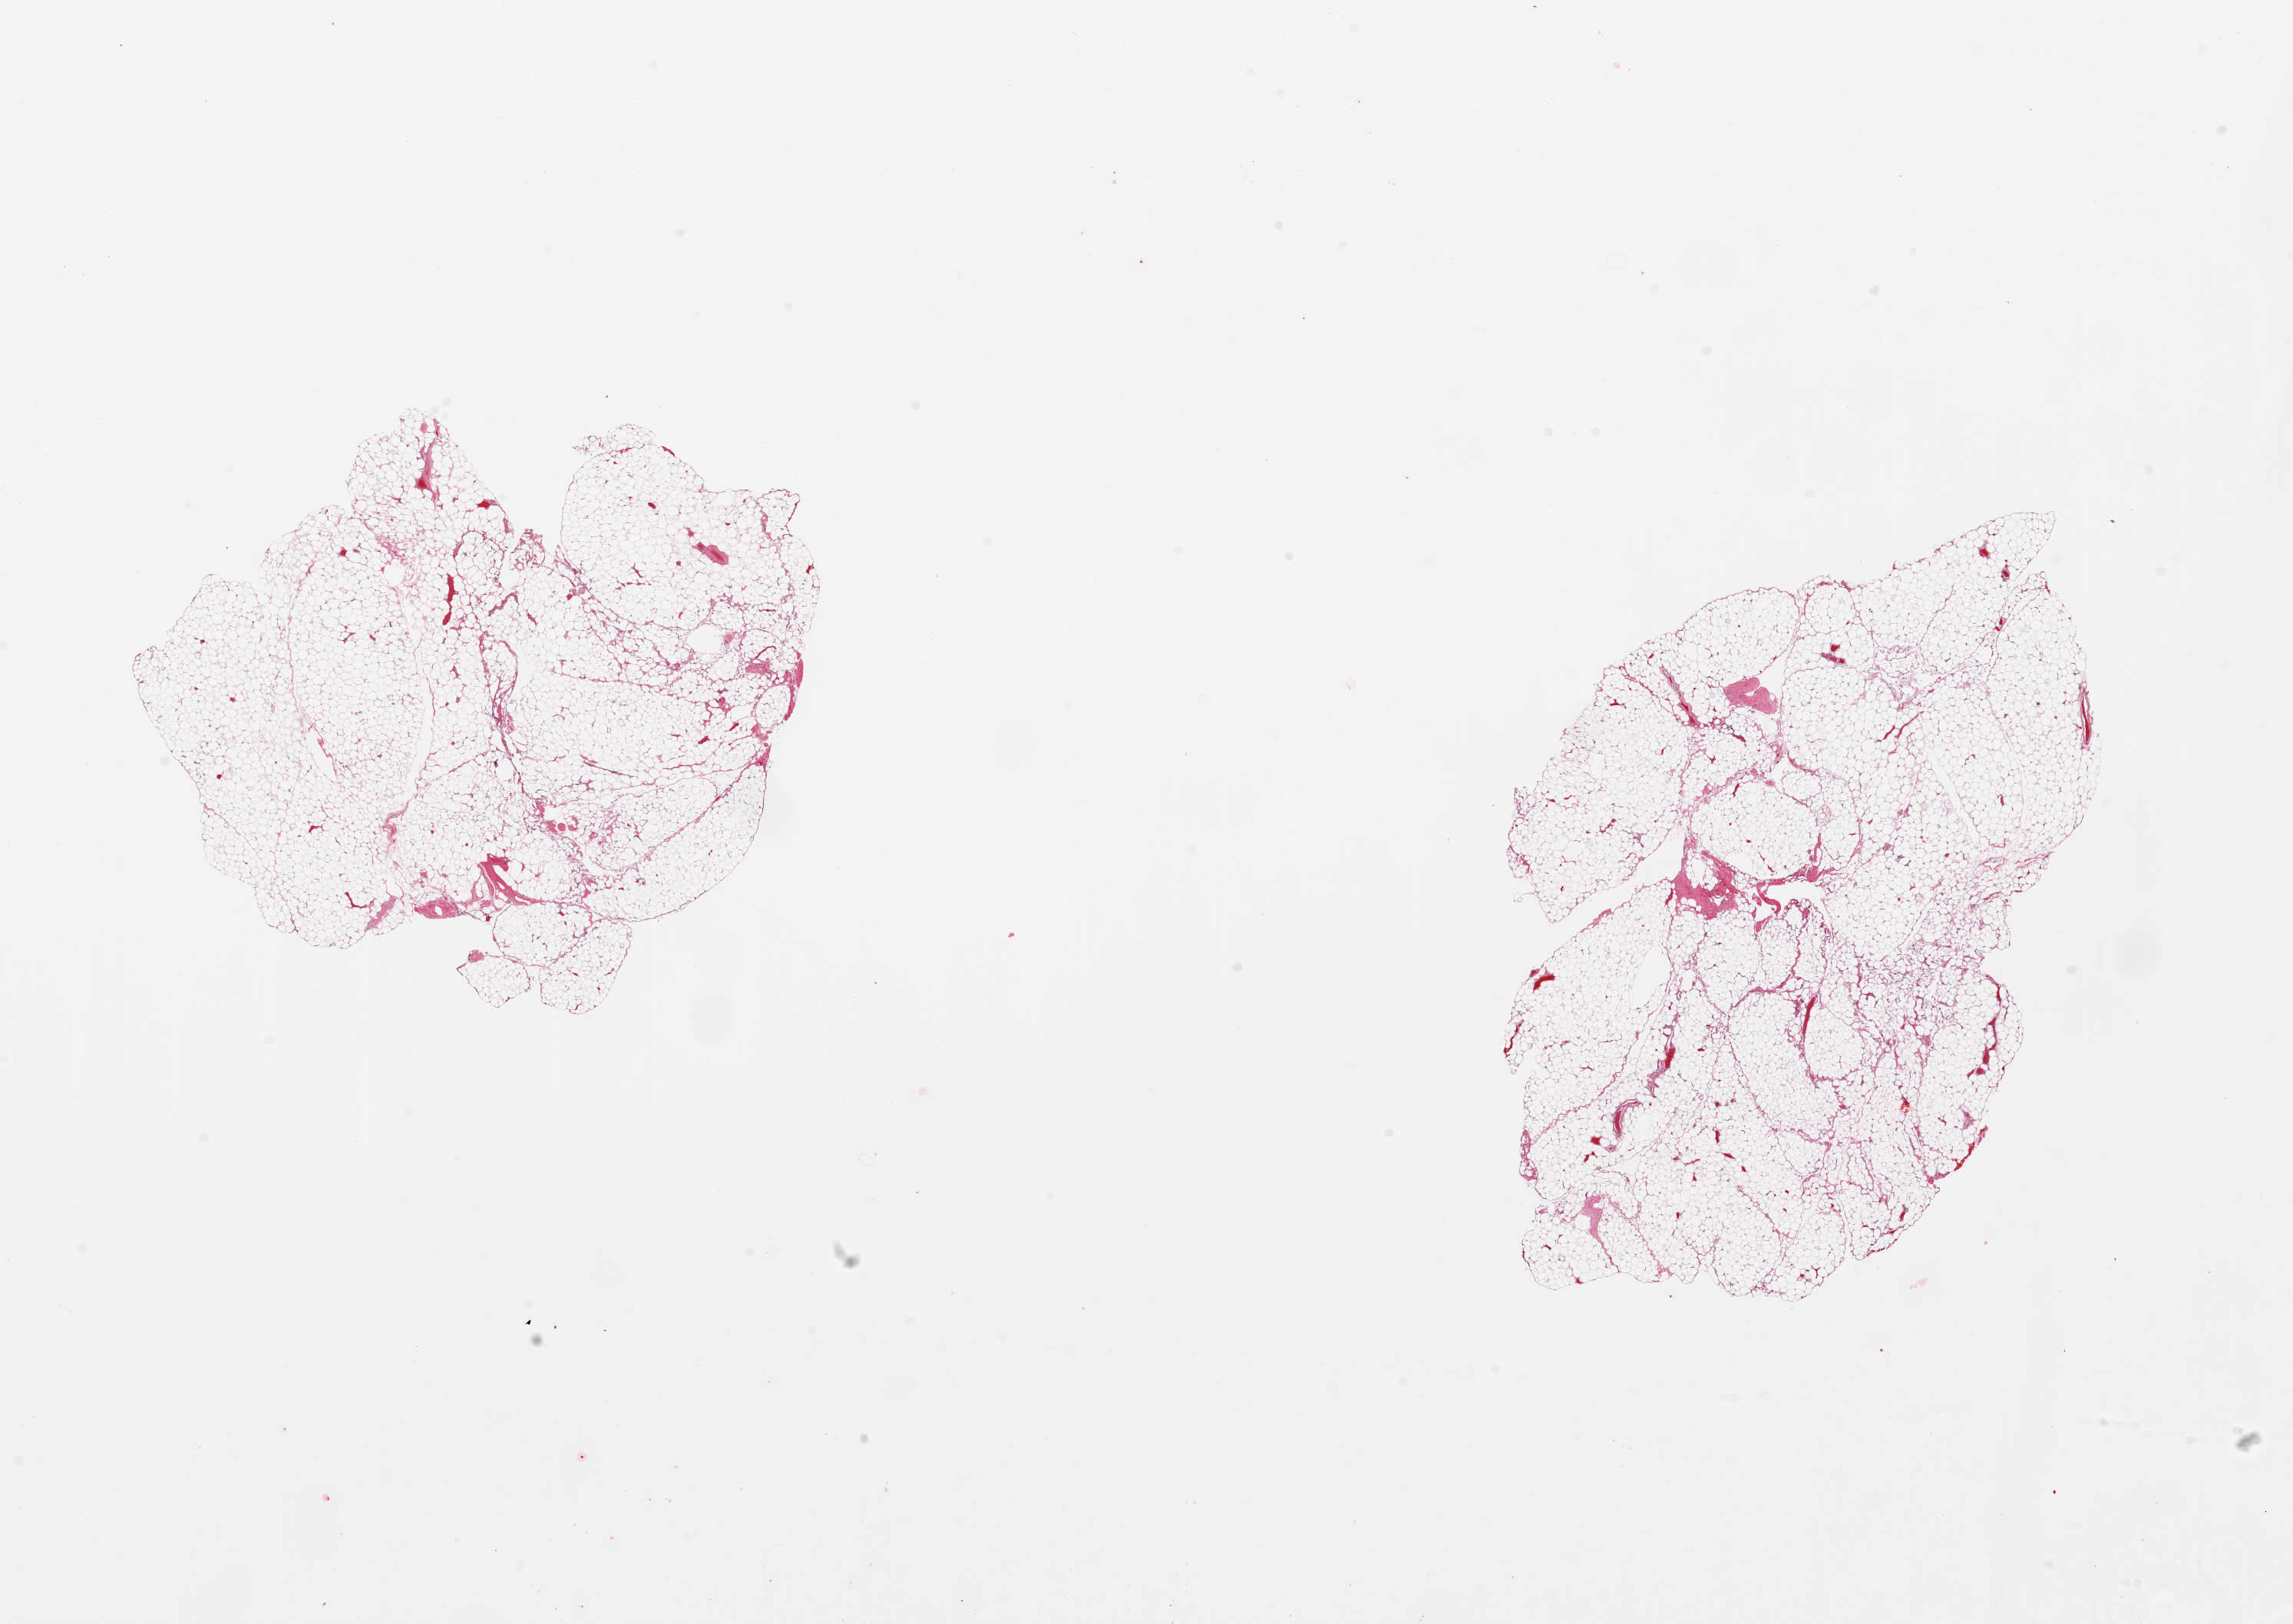
Whole-slide image, haematoxylin and eosin stain, brightfield, low-resolution overview of the scanned area, about 23.6 x 16.7 mm; PAXgene-fixed paraffin-embedded (PFPE) section; section of omentum (target tissue); donor tissue sample. Female donor.
* reviewer comment on this tissue sample: 2 pieces